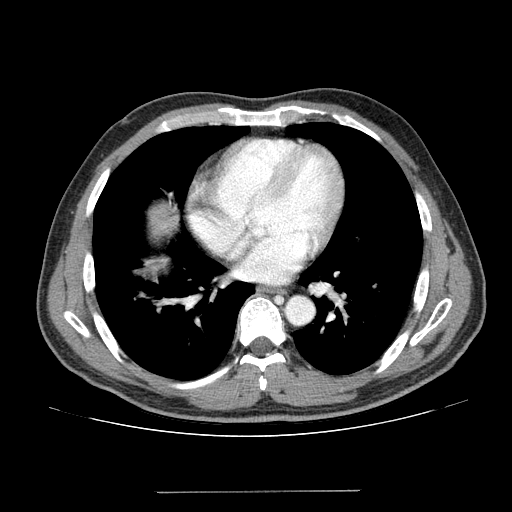
Contrast-enhanced abdominal CT (liver protocol), one axial slice. Position 126 of 131 along the scan axis. Reconstruction kernel STANDARD. One of 2 acquisitions stored at this slice position. Soft-tissue window (W 400 / L 40 HU). 2.5 mm slice thickness. 512 × 512 image matrix, field of view 380 × 380 mm. Case-level facts recorded for this patient, not image findings: diagnosis: hepatocellular carcinoma (patient treated with transarterial chemoembolisation; whether this scan precedes or follows treatment is not stated here); TNM stage (as recorded): Stage-I; Child-Pugh class: A; tumour differentiation: poorly differentiated; tumour nodularity: uninodular.
Outlined on this slice (semi-automatic segmentation, software-assisted and operator-edited):
- liver parenchyma outside the tumour (the mass and vessels are separate outlines, so this box may not span the whole liver): bounding box (x1, y1, x2, y2) in pixels: (146, 204, 178, 272)